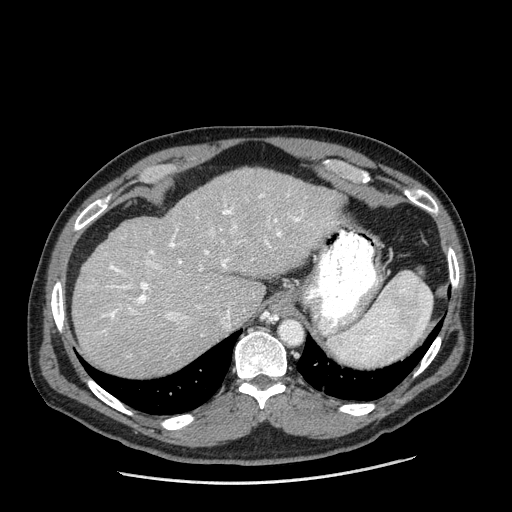
Contrast-enhanced abdominal CT (liver protocol), one axial slice. Position 141 of 198 along the scan axis. Reconstruction kernel STANDARD. One of 2 acquisitions stored at this slice position. Soft-tissue window (W 400 / L 40 HU). 2.5 mm slice thickness. 512 × 512 image matrix, field of view 400 × 400 mm. Case-level facts recorded for this patient, not image findings: diagnosis: hepatocellular carcinoma (patient treated with transarterial chemoembolisation; whether this scan precedes or follows treatment is not stated here); TNM stage (as recorded): Stage-II; Child-Pugh class: A; tumour nodularity: multinodular; tumour size: 2.6 cm.
Outlined on this slice (semi-automatically segmented with operator editing):
- liver parenchyma outside the tumour (the mass and vessels are separate outlines, so this box may not span the whole liver): bounding box <72,168,340,376> (left, top, right, bottom; pixels)
- liver vessels: <102,194,304,336>